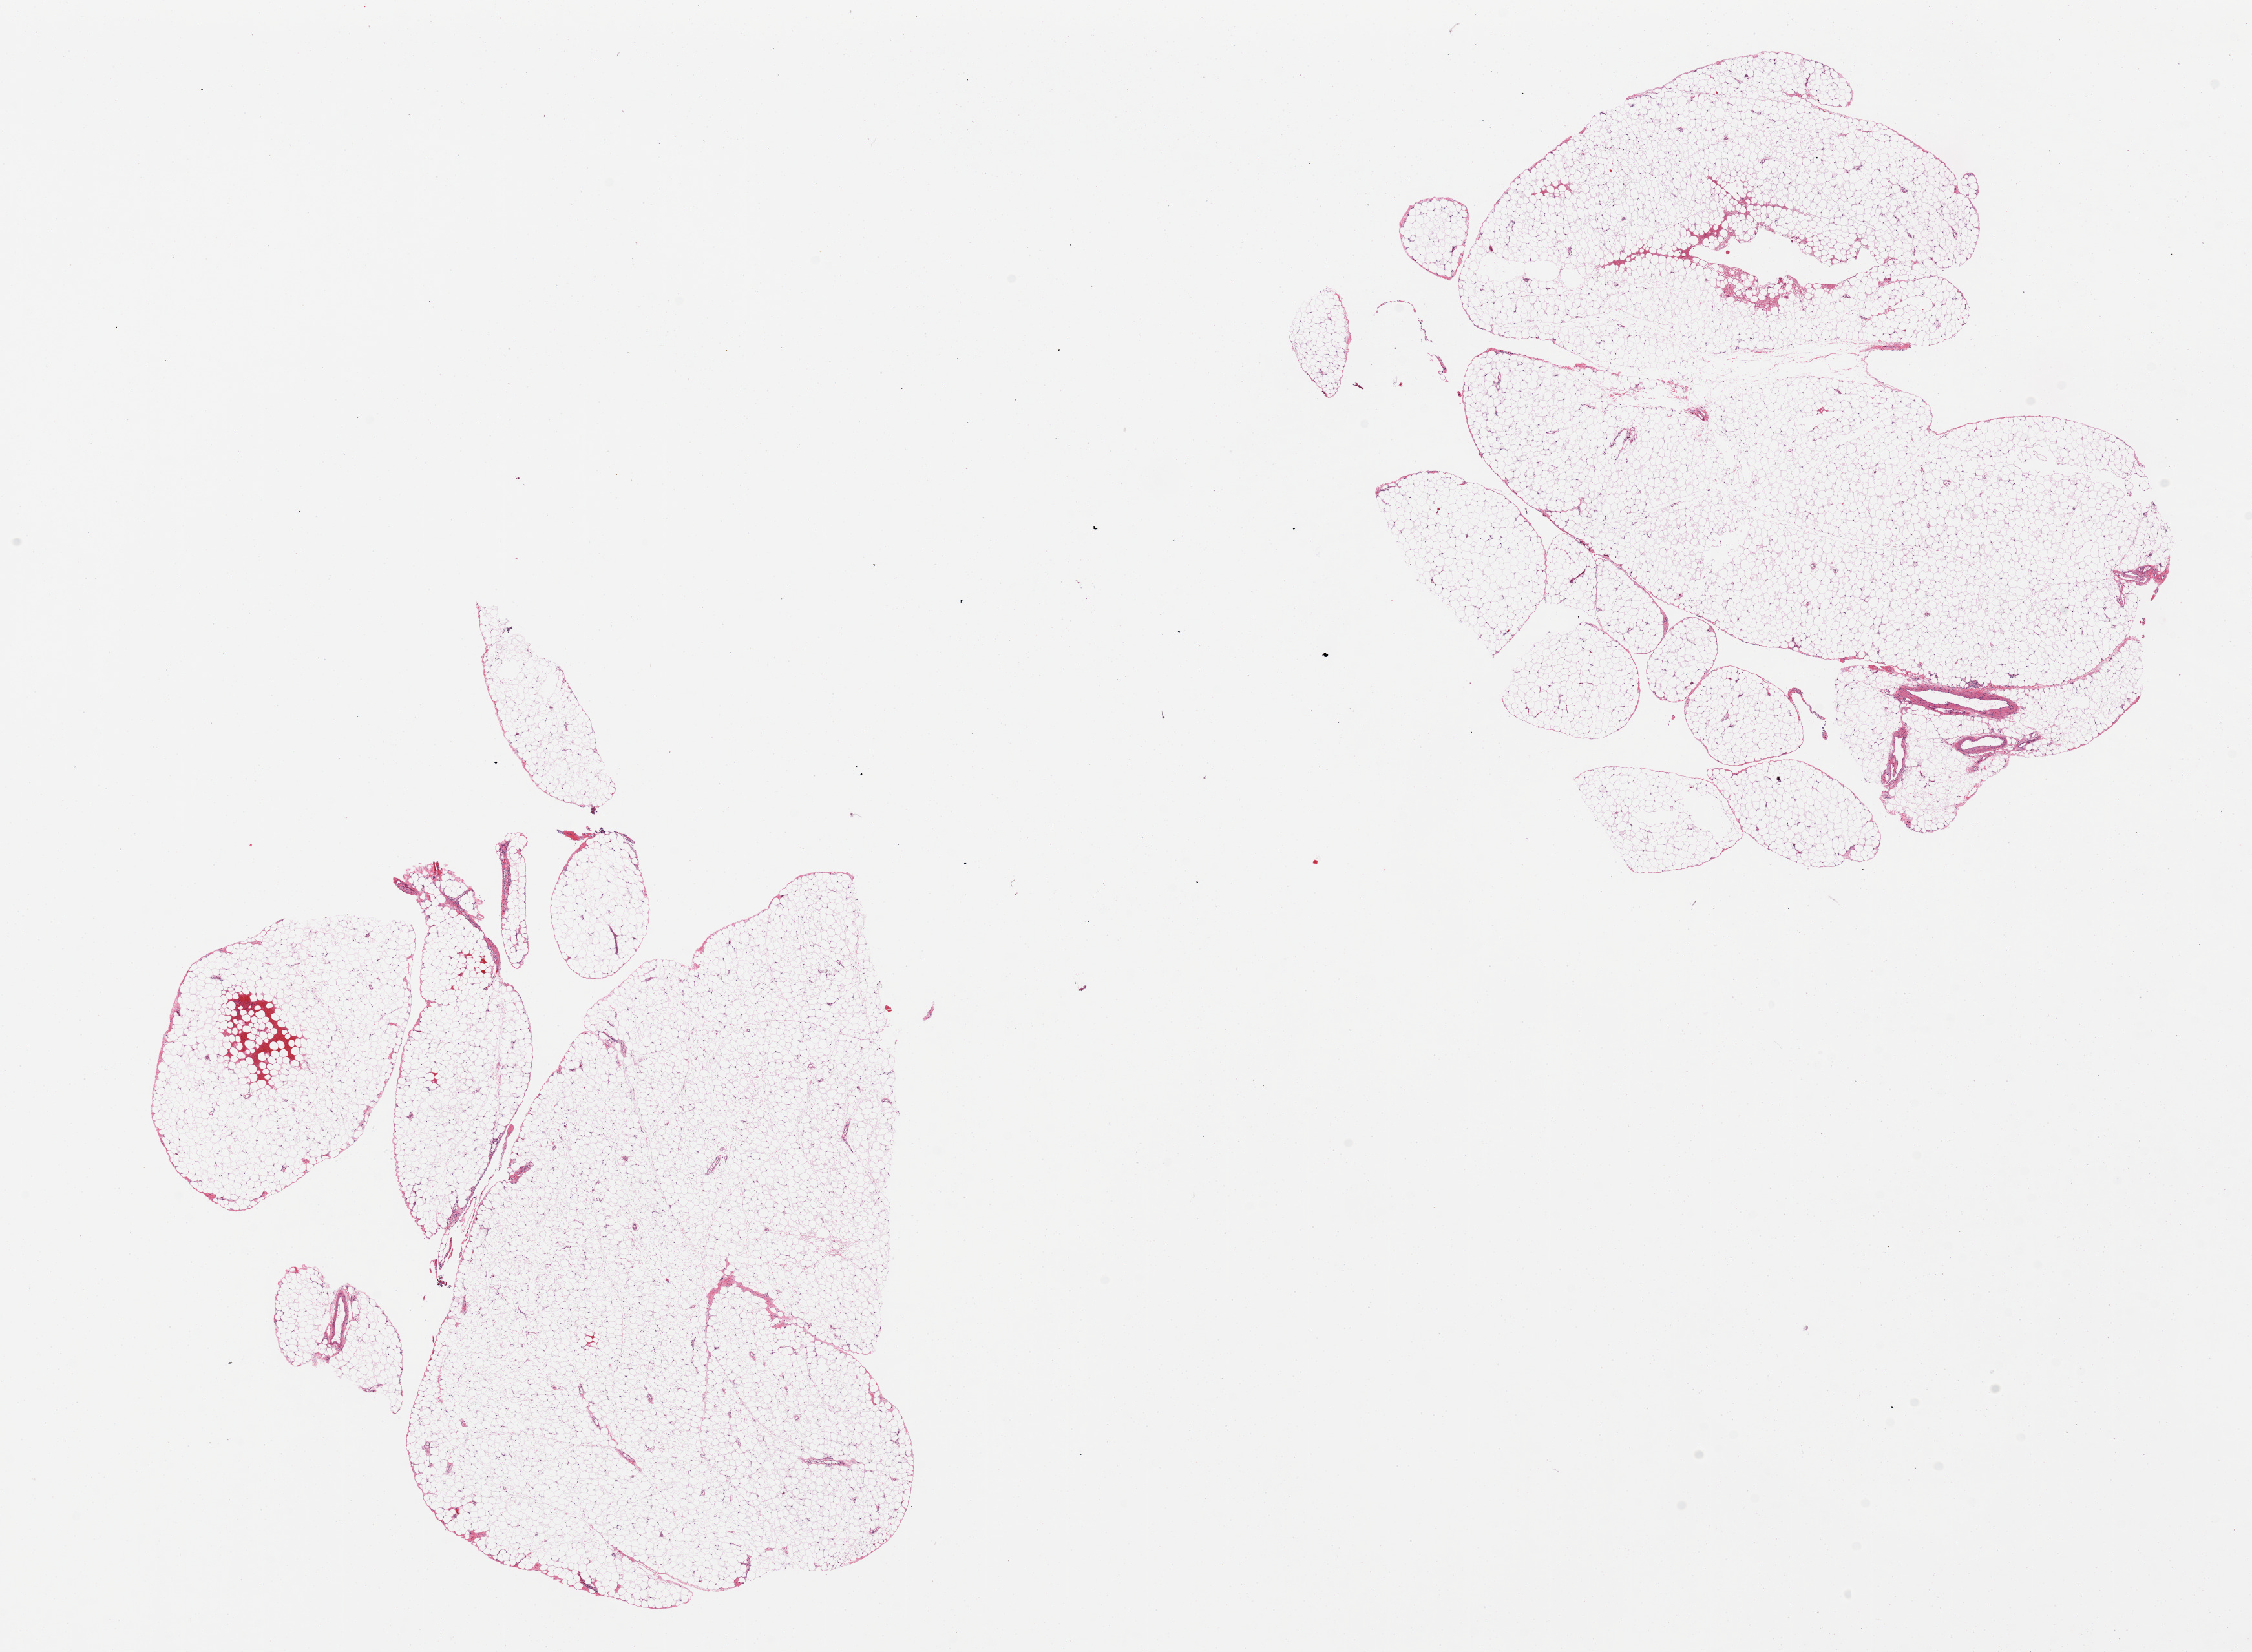
Digitized haematoxylin and eosin-stained section — whole scanned area (about 27.6 x 20.2 mm) shown as a low-resolution overview. PAXgene-fixed paraffin-embedded (PFPE) section. Target tissue: omentum. Donor tissue sample. Donor: female.
Reviewer comment on this tissue sample: 2 pieces.